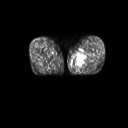
FDG PET of an extremity soft-tissue mass (from a PET/CT study), one axial slice. Slice 13 of 267 in the series (ordered by position). 3.27 mm slice thickness. 128 × 128 image matrix, field of view 600 × 600 mm. Male patient, age 59 years. From the clinical record (not read from this slice): histological type: pleiomorphic liposarcoma; grade: high; site of the primary tumour: left thigh.
Structures marked on this image (expert contour drawn on MRI and transferred to this co-registered scan by the dataset authors):
- gross tumour volume including surrounding oedema: box from (x=76, y=52) to (x=89, y=68) px
- gross tumour volume (mass): (x=80, y=63)–(x=82, y=64)